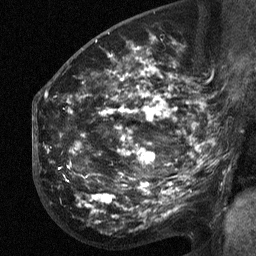
Breast MRI (dynamic contrast-enhanced), one sagittal slice; position 35 of 64 along the scan axis; dynamic contrast-enhanced study with each time point stored as its own series, time point 2 of 3 at this slice position (early post-contrast, ordered by acquisition time); 1.5 T; TE 4.8 ms, TR 27 ms; 2.3 mm slice thickness; 256 × 256 image matrix, field of view 200 × 200 mm. Patient: female, 50 years. From the clinical record (not read from this slice): setting: breast cancer imaged before/during neoadjuvant chemotherapy; receptor status: HER2-positive.
Annotated regions visible in this slice (semi-automatically segmented with operator editing):
- analysis volume of interest (the breast-tissue region the enhancement analysis was run in; not a lesion): box from (x=53, y=64) to (x=211, y=216) px
- tumour enhancement mask (voxels above the 90 % enhancement threshold inside the analysis volume of interest): (x=72, y=66)–(x=198, y=164)